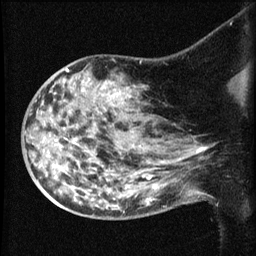
Breast MRI (dynamic contrast-enhanced), one sagittal slice; dynamic contrast-enhanced series, image 2 of 3 at this slice position (ordered by acquisition); 1.5 T; TE 4.2 ms, TR 8.2 ms; 256 × 256 image matrix. Patient: female, 50 years.
Outlined on this slice (semi-automatic segmentation, software-assisted and operator-edited):
- analysis volume of interest (the breast-tissue region the enhancement analysis was run in; not a lesion): bounding box <38,75,169,211> (left, top, right, bottom; pixels)
- tumour enhancement mask (voxels above the 70 % enhancement threshold inside the analysis volume of interest): <142,175,147,178>